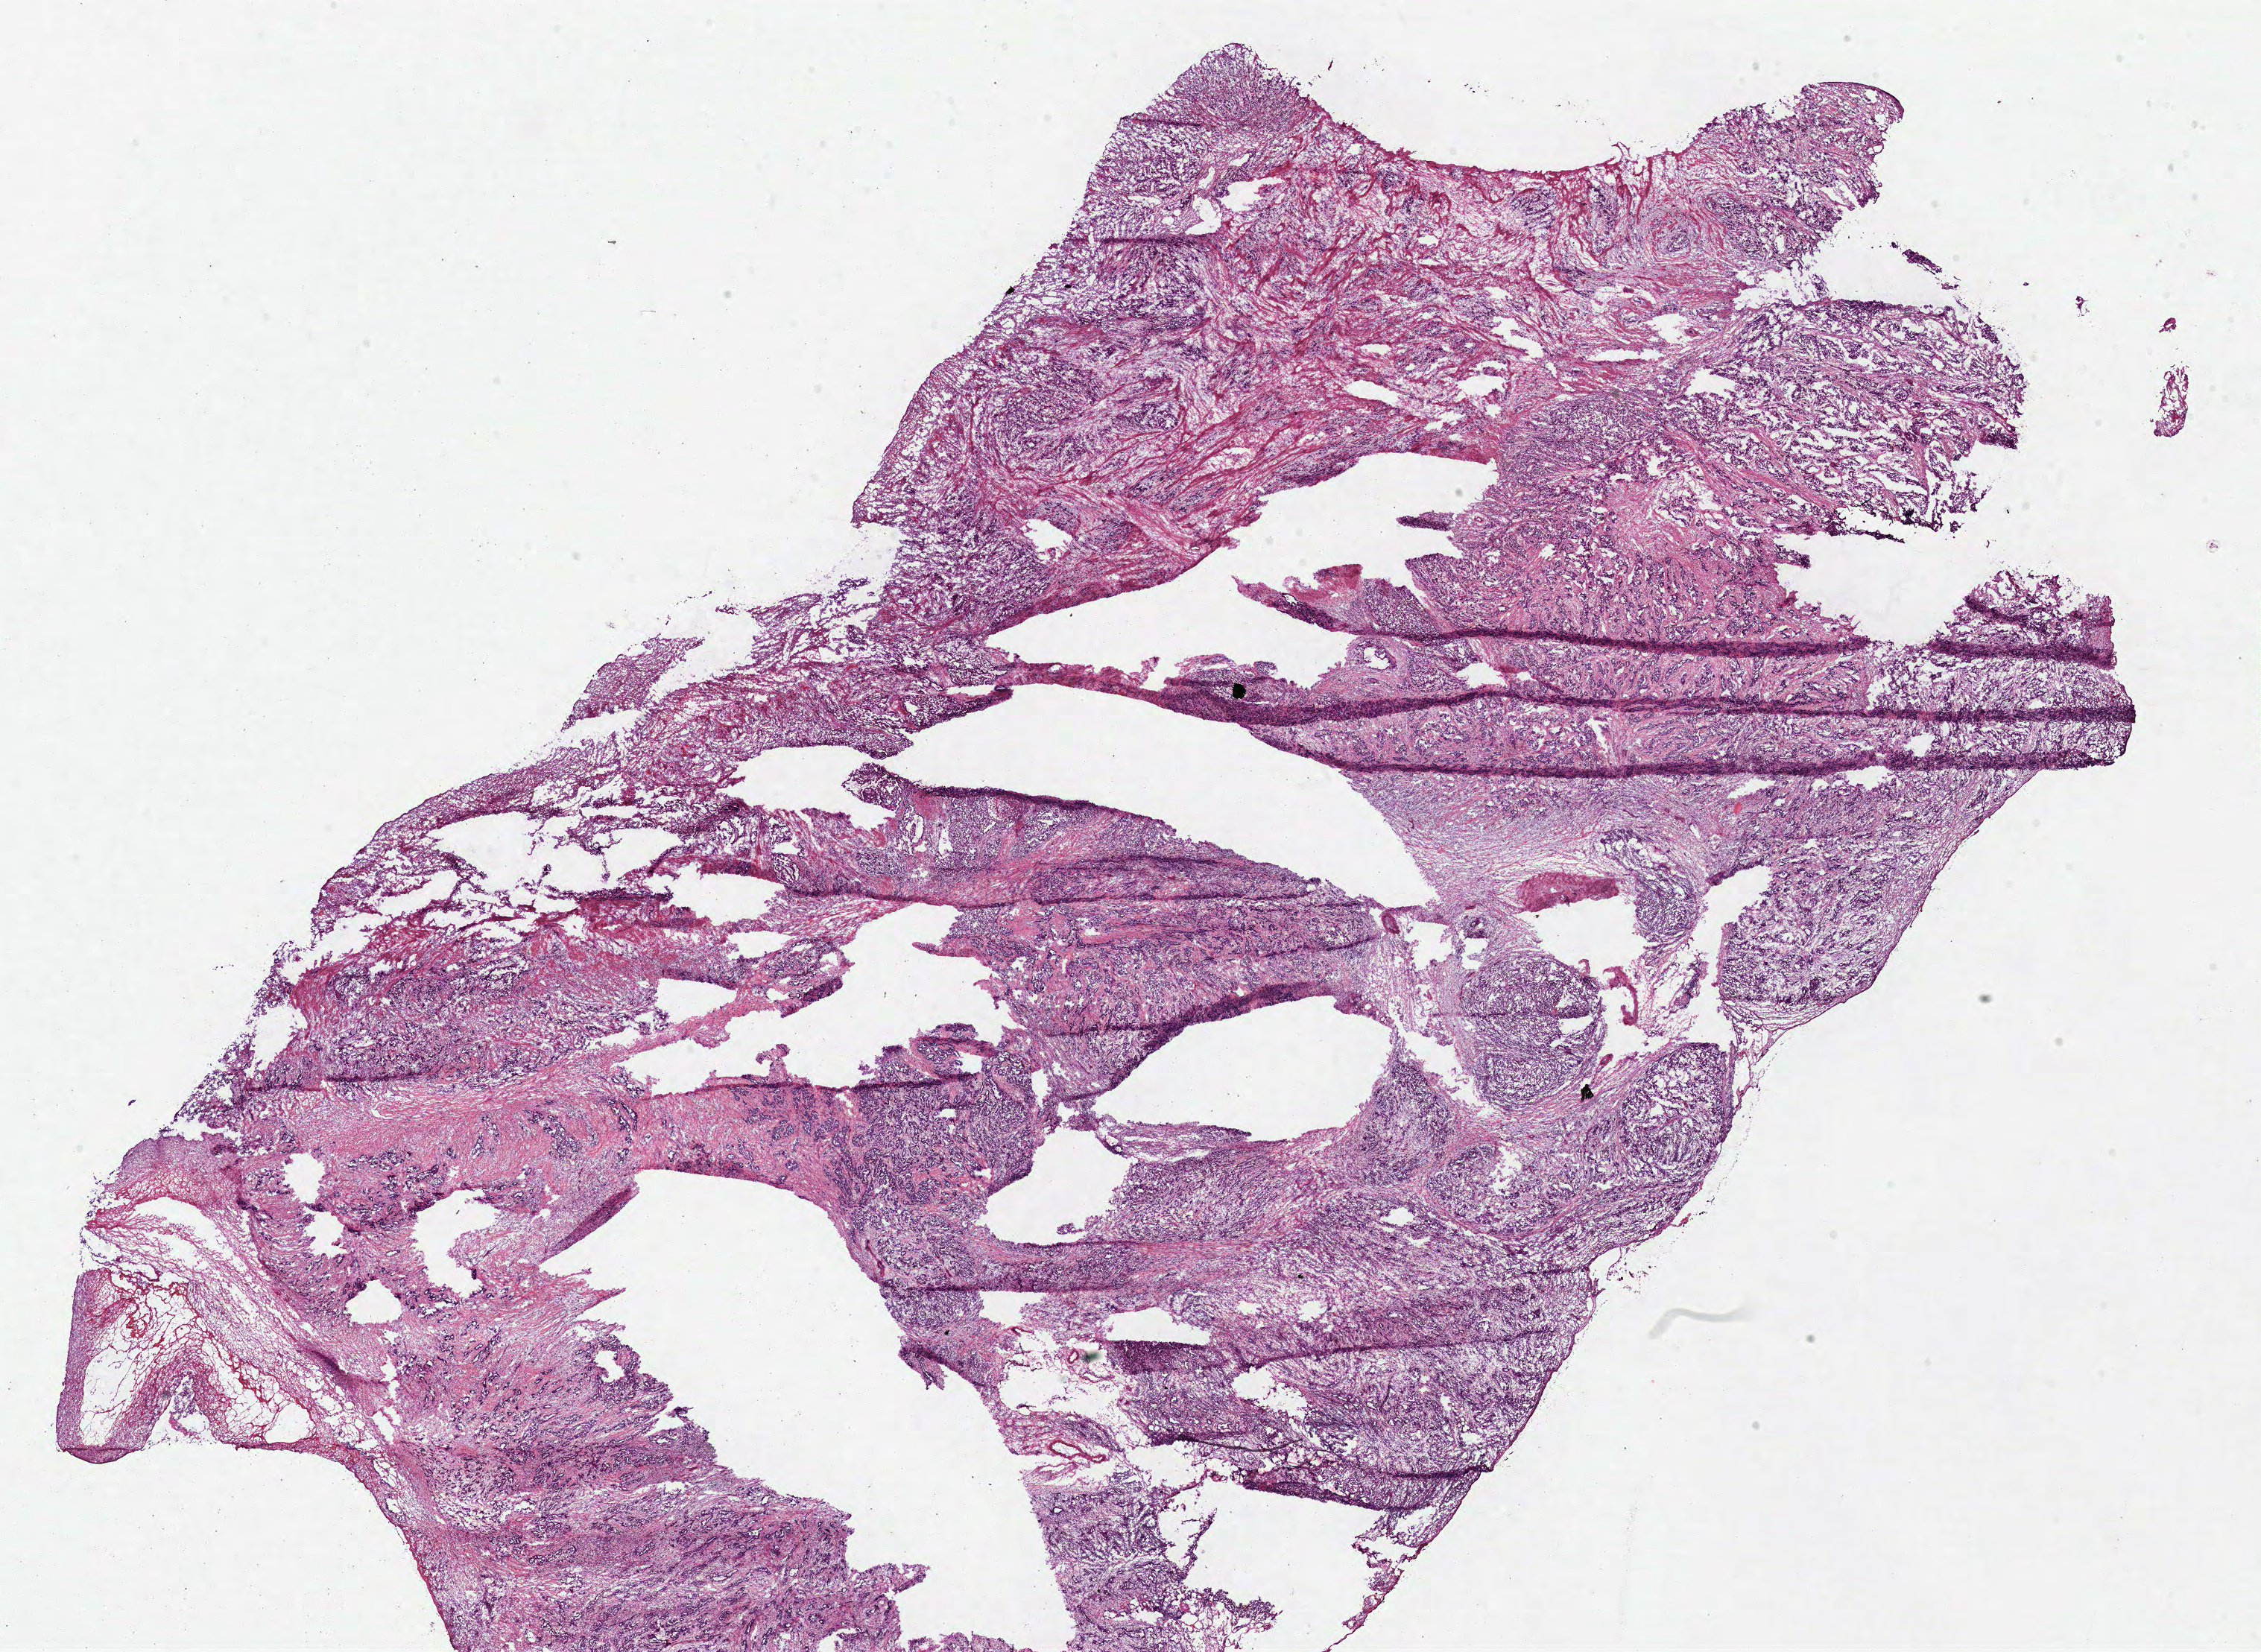
Digitized H&E tissue section (whole slide) — whole scanned area (about 23.9 x 17.5 mm, from a 40x scan) shown as a low-resolution overview. Frozen section from the bottom of the tissue portion. Stomach, primary tumour sample. Female patient; age at initial diagnosis 57 years. Histologic grade: G3 (poorly differentiated). Composition of this section per pathologist review: tumour cells 100%, tumour nuclei 75%, normal cells 0%, stromal cells 0%, necrosis 0%. Inflammatory infiltration, as recorded: lymphocyte infiltration 10%, monocyte infiltration 0%, neutrophil infiltration 5%.
TNM: T3 N1 M0. Pathologic diagnosis: Adenocarcinoma, NOS (body of stomach). AJCC pathologic stage: IIB (7th edition).